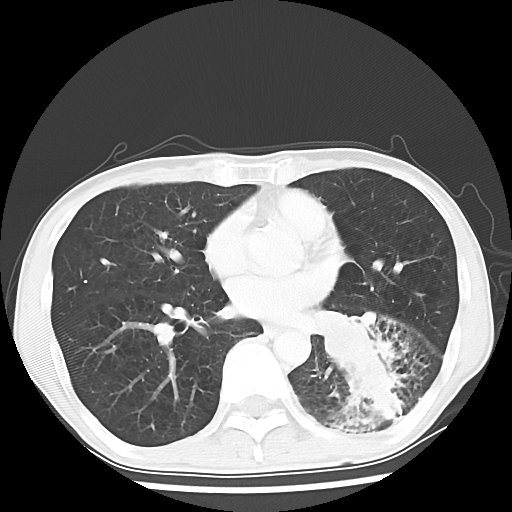
Chest CT, one axial slice; reconstruction kernel LUNG; 120 kVp; lung window (W 1500 / L -600 HU); 5 mm slice thickness; 512 × 512 image matrix, field of view 313 × 313 mm. Patient: male, 68 years. From the clinical record (not read from this slice): clinical TNM (as recorded): T4 N0 M0.
Outlined on this slice (rectangle marked by the reading radiologist):
- lung tumour (recorded histology: squamous cell carcinoma): box from (x=318, y=303) to (x=410, y=425) px